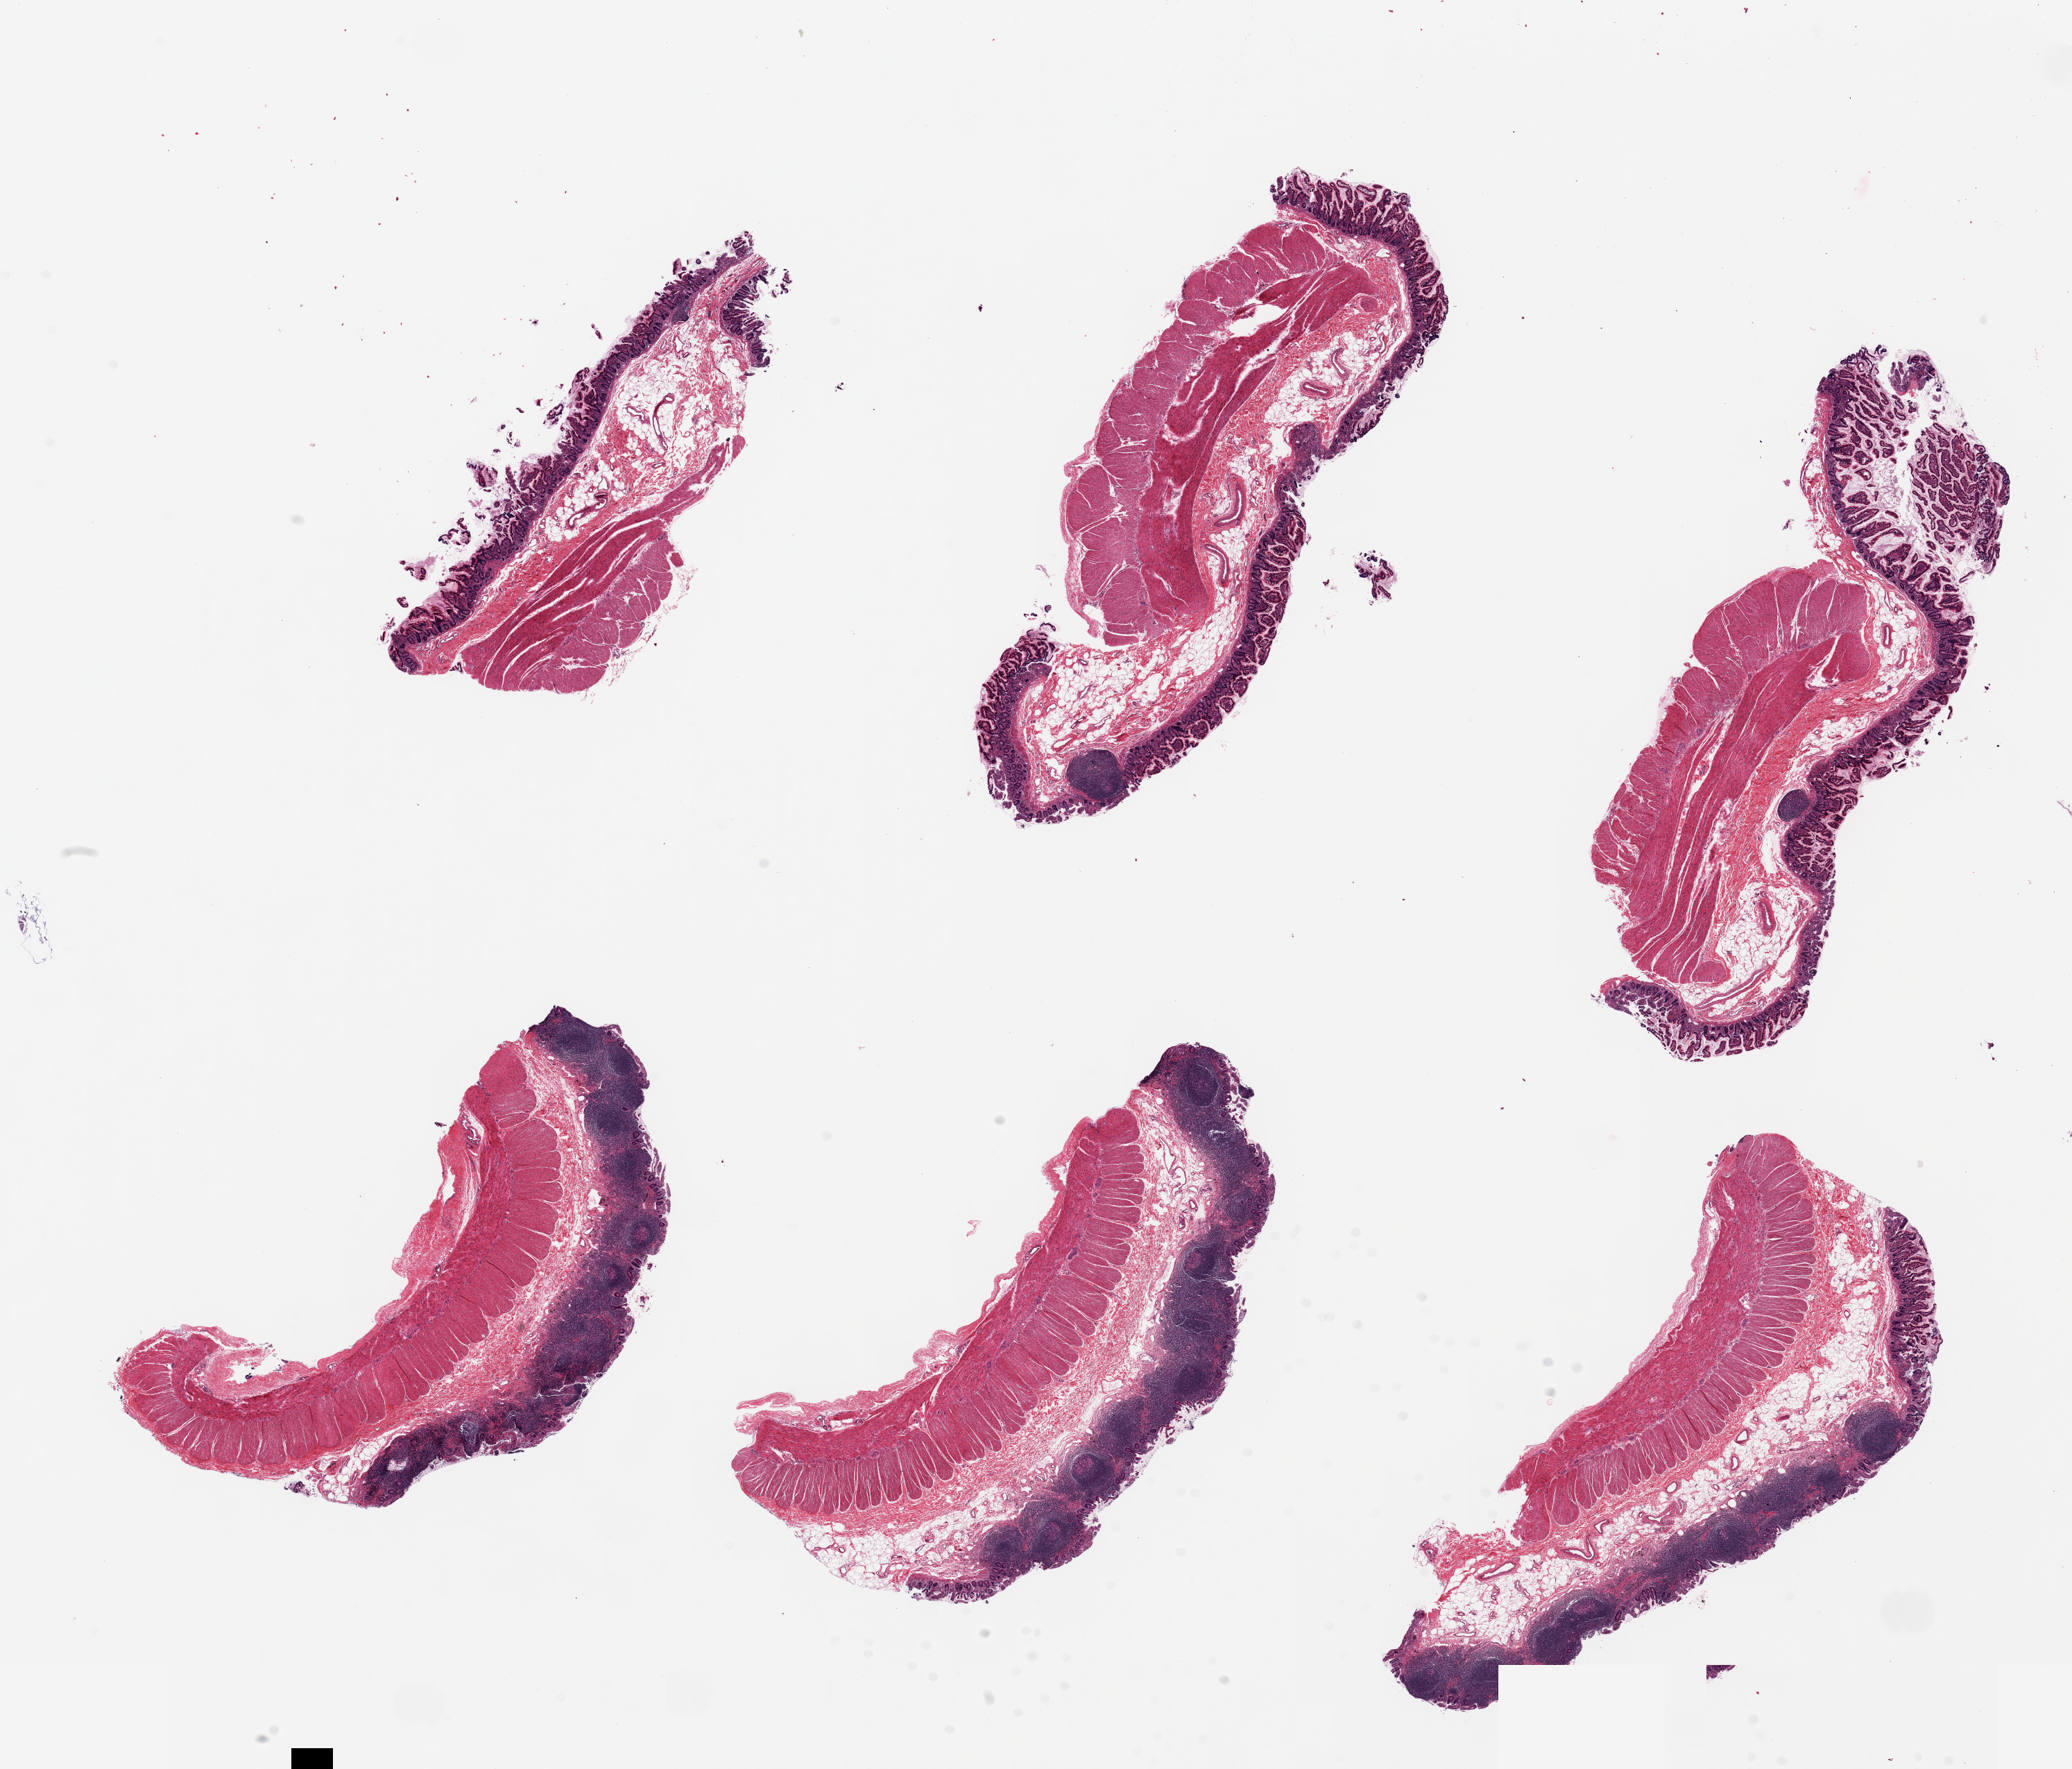
Digitized H&E-stained section, brightfield — whole scanned area (about 23.6 x 20.2 mm, acquisition: 20x scan) shown as a low-resolution overview, PAXgene-fixed paraffin-embedded (PFPE) section, target tissue: ileum, tissue donor sample. Donor: male.
Review note (as recorded): 6 pieces ~7x2.5mm; 50% show good lymphoid areas up to ~20% of thickness; Still abundant muscle attached.